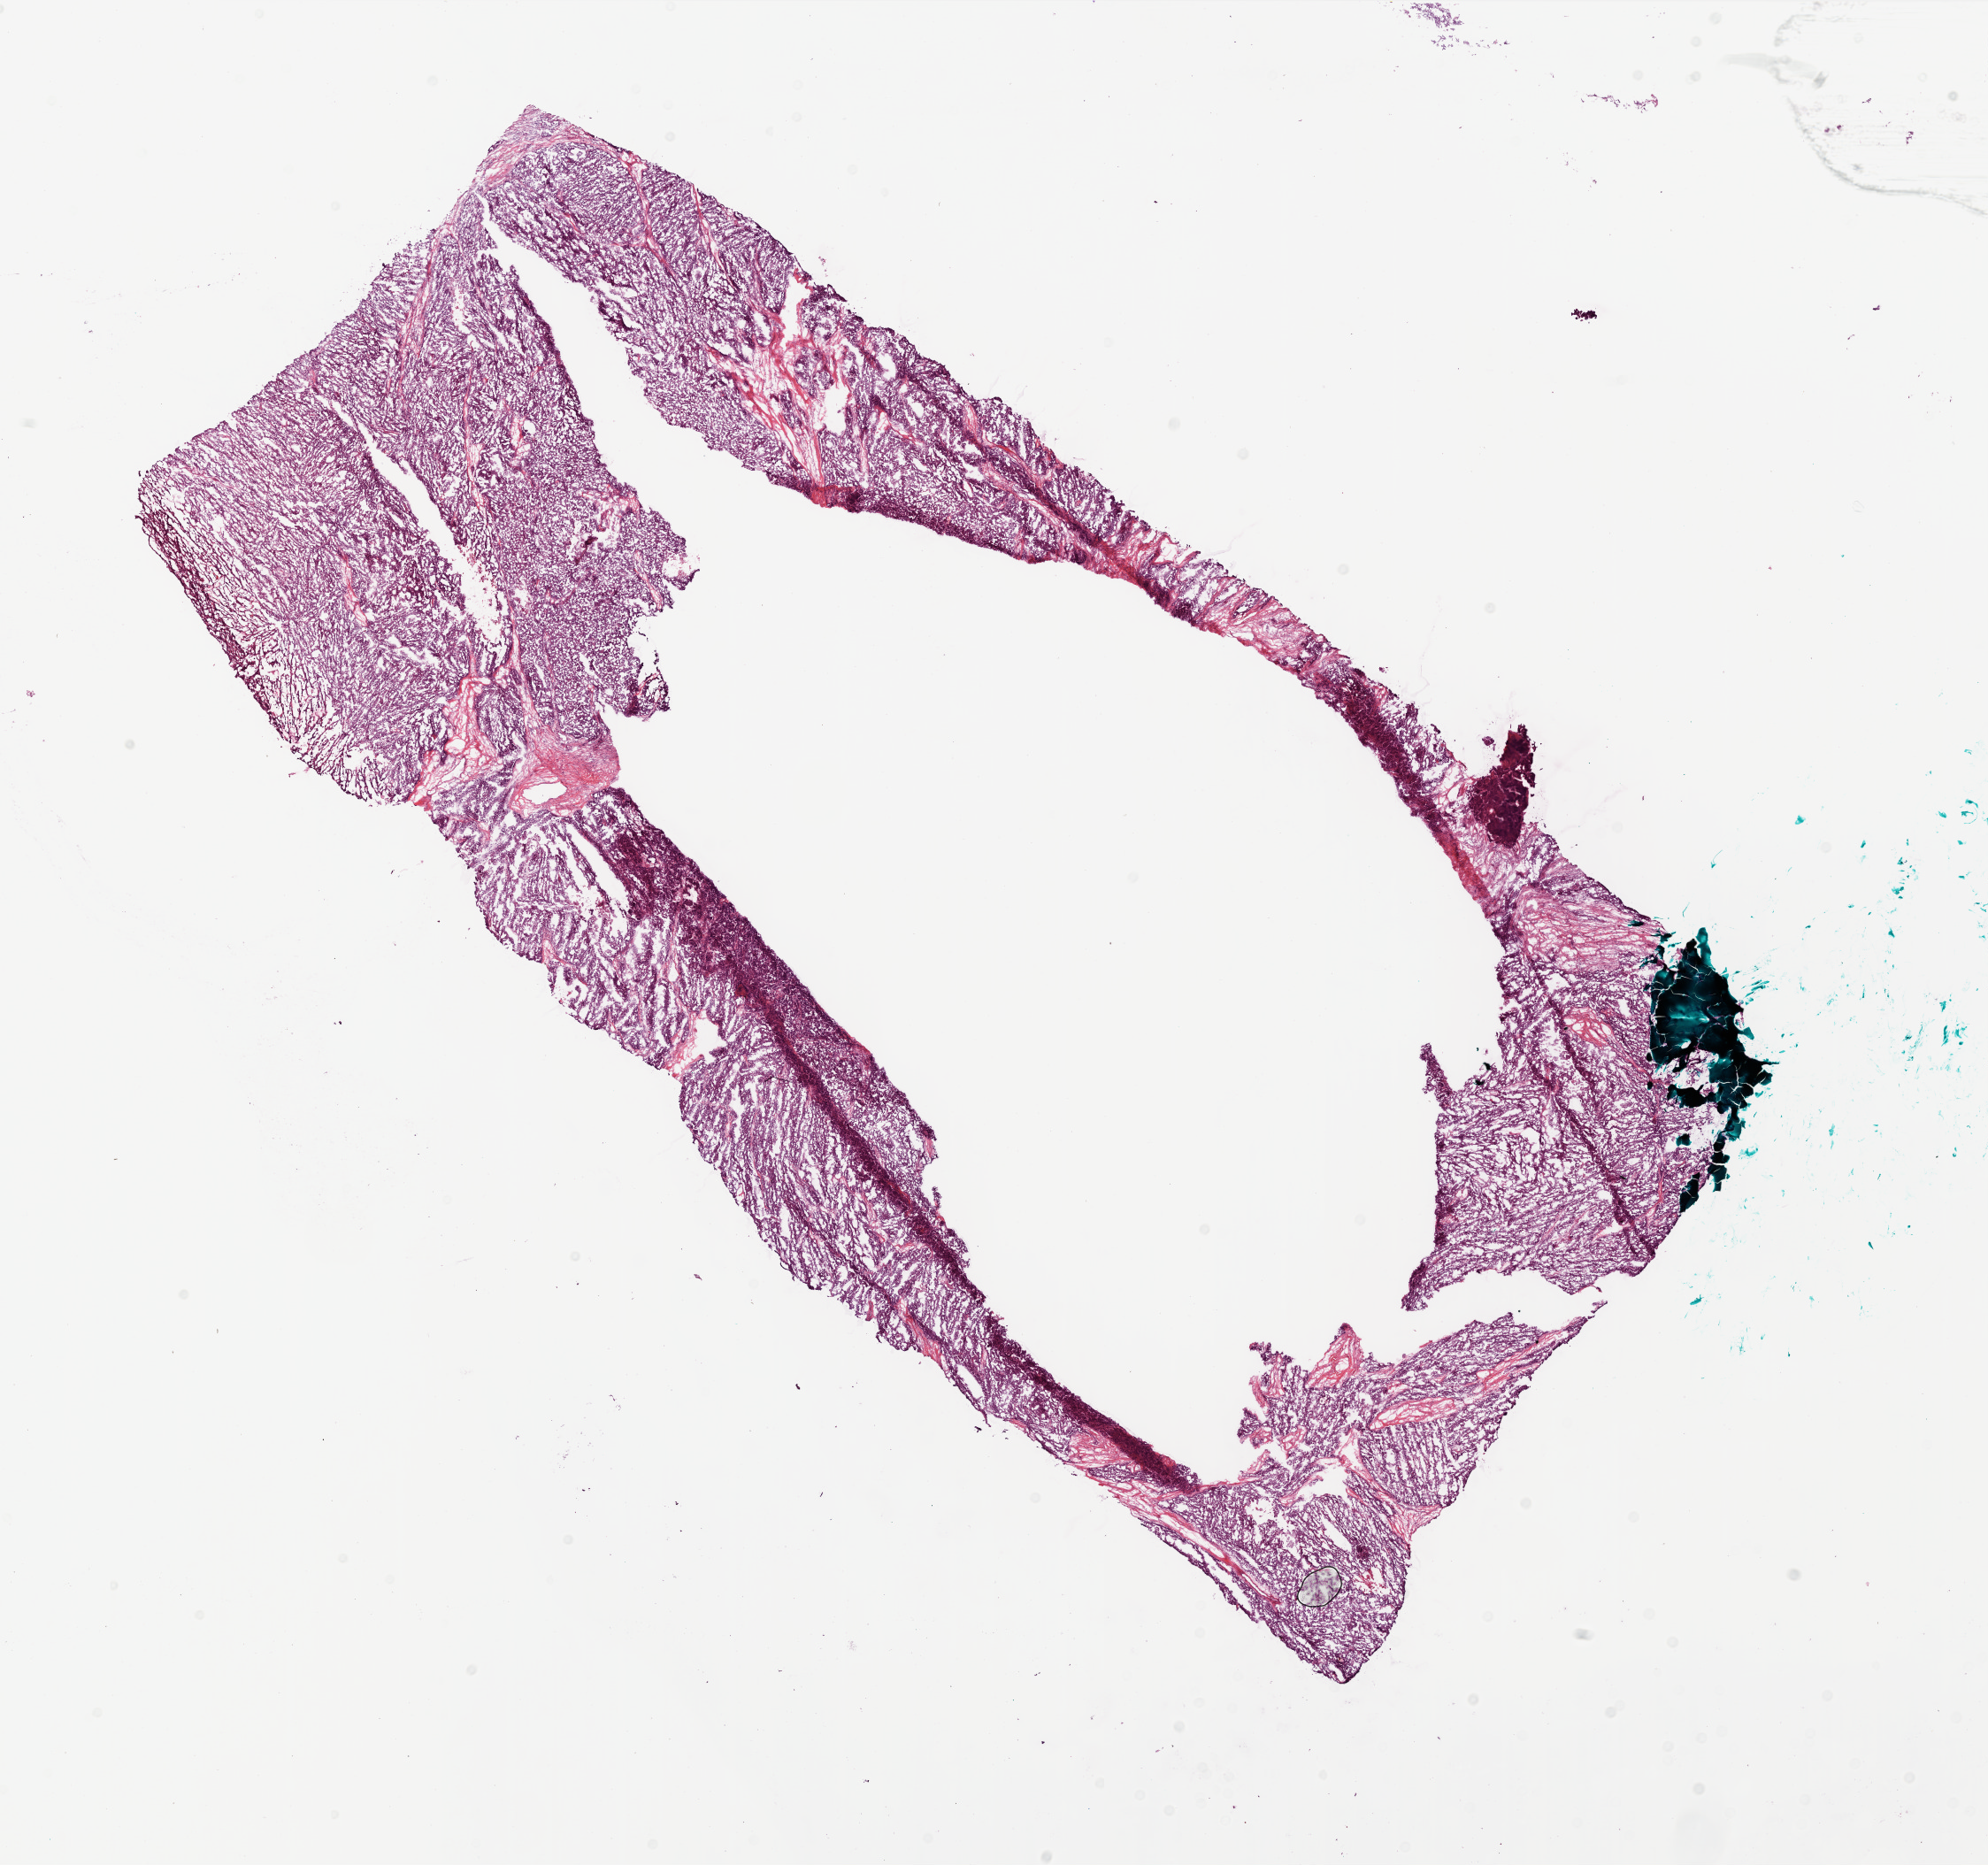
Hematoxylin and eosin (H&E) stained whole-slide image, low-resolution overview of the scanned area, about 18.0 x 16.9 mm (slide scanned at 20x). Frozen section. Primary tumour sample from the ovary. Patient: female, age at initial diagnosis 63 years. Histologic grade: G3 (poorly differentiated). Pathologist review of this section (percent, as recorded): tumour cells 90%, tumour nuclei 91%, normal cells 8%, stromal cells 1%, necrosis 1%. Inflammatory infiltration, as recorded: lymphocyte infiltration 50%.
* histologic diagnosis: Serous cystadenocarcinoma, NOS
* FIGO stage: IIIC